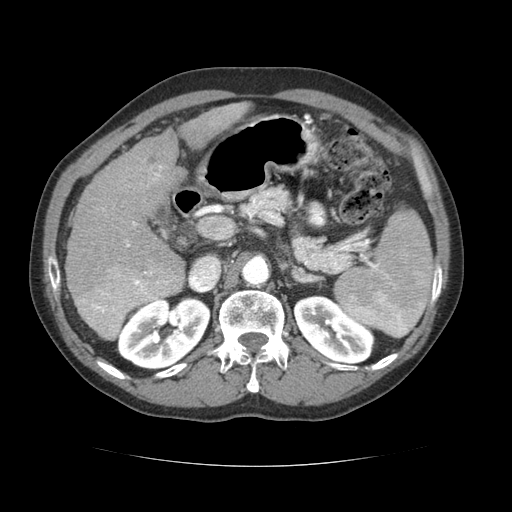
Contrast-enhanced abdominal CT (liver protocol), one axial slice; position 39 of 69 along the scan axis; reconstruction kernel STANDARD; 120 kVp; soft-tissue window (W 400 / L 40 HU); 2.5 mm slice thickness; 512 × 512 image matrix, field of view 360 × 360 mm. Case-level facts recorded for this patient, not image findings: diagnosis: hepatocellular carcinoma (patient treated with transarterial chemoembolisation; whether this scan precedes or follows treatment is not stated here); TNM stage (as recorded): Stage-II.
Structures marked on this image (semi-automatically segmented with operator editing):
- liver parenchyma outside the tumour (the mass and vessels are separate outlines, so this box may not span the whole liver): bounding box <64,102,248,327> (left, top, right, bottom; pixels)
- mass: <78,263,182,341>
- liver vessels: <126,166,162,247>